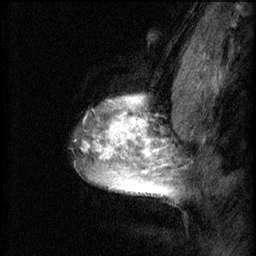
Breast MRI (dynamic contrast-enhanced), one sagittal slice; slice 49 of 60 in the series (ordered by position); 3 images stored at this slice position (order not interpretable as contrast timing); 1.5 T; TE 4.2 ms, TR 8.2 ms; 256 × 256 image matrix, field of view 180 × 180 mm. Patient: female, 40 years.
Annotated regions visible in this slice (semi-automatically segmented with operator editing):
- analysis volume of interest (the breast-tissue region the enhancement analysis was run in; not a lesion): bounding box [x1, y1, x2, y2] px = [72, 82, 167, 197]
- tumour enhancement mask (voxels above the 70 % enhancement threshold inside the analysis volume of interest): [84, 94, 167, 197]